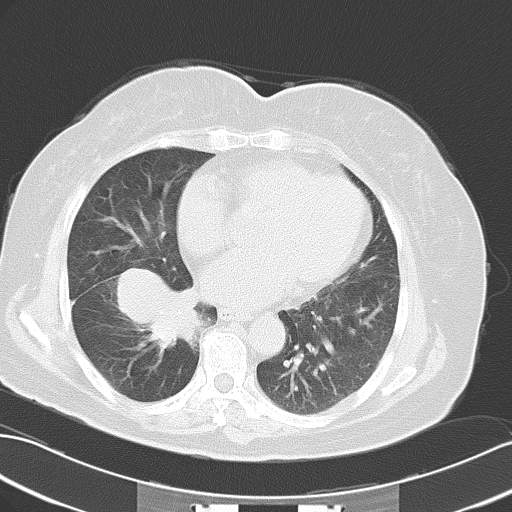
Chest CT, one axial slice; position 22 of 50 along the scan axis; reconstruction kernel B70f; lung window (W 1500 / L -600 HU); 512 × 512 image matrix. Patient: female, 63 years. Case-level facts recorded for this patient, not image findings: clinical TNM (as recorded): T3 N0 M0.
Structures marked on this image (bounding box drawn by a radiologist):
- lung tumour (recorded histology: adenocarcinoma): bounding box (x1, y1, x2, y2) in pixels: (107, 267, 201, 352)